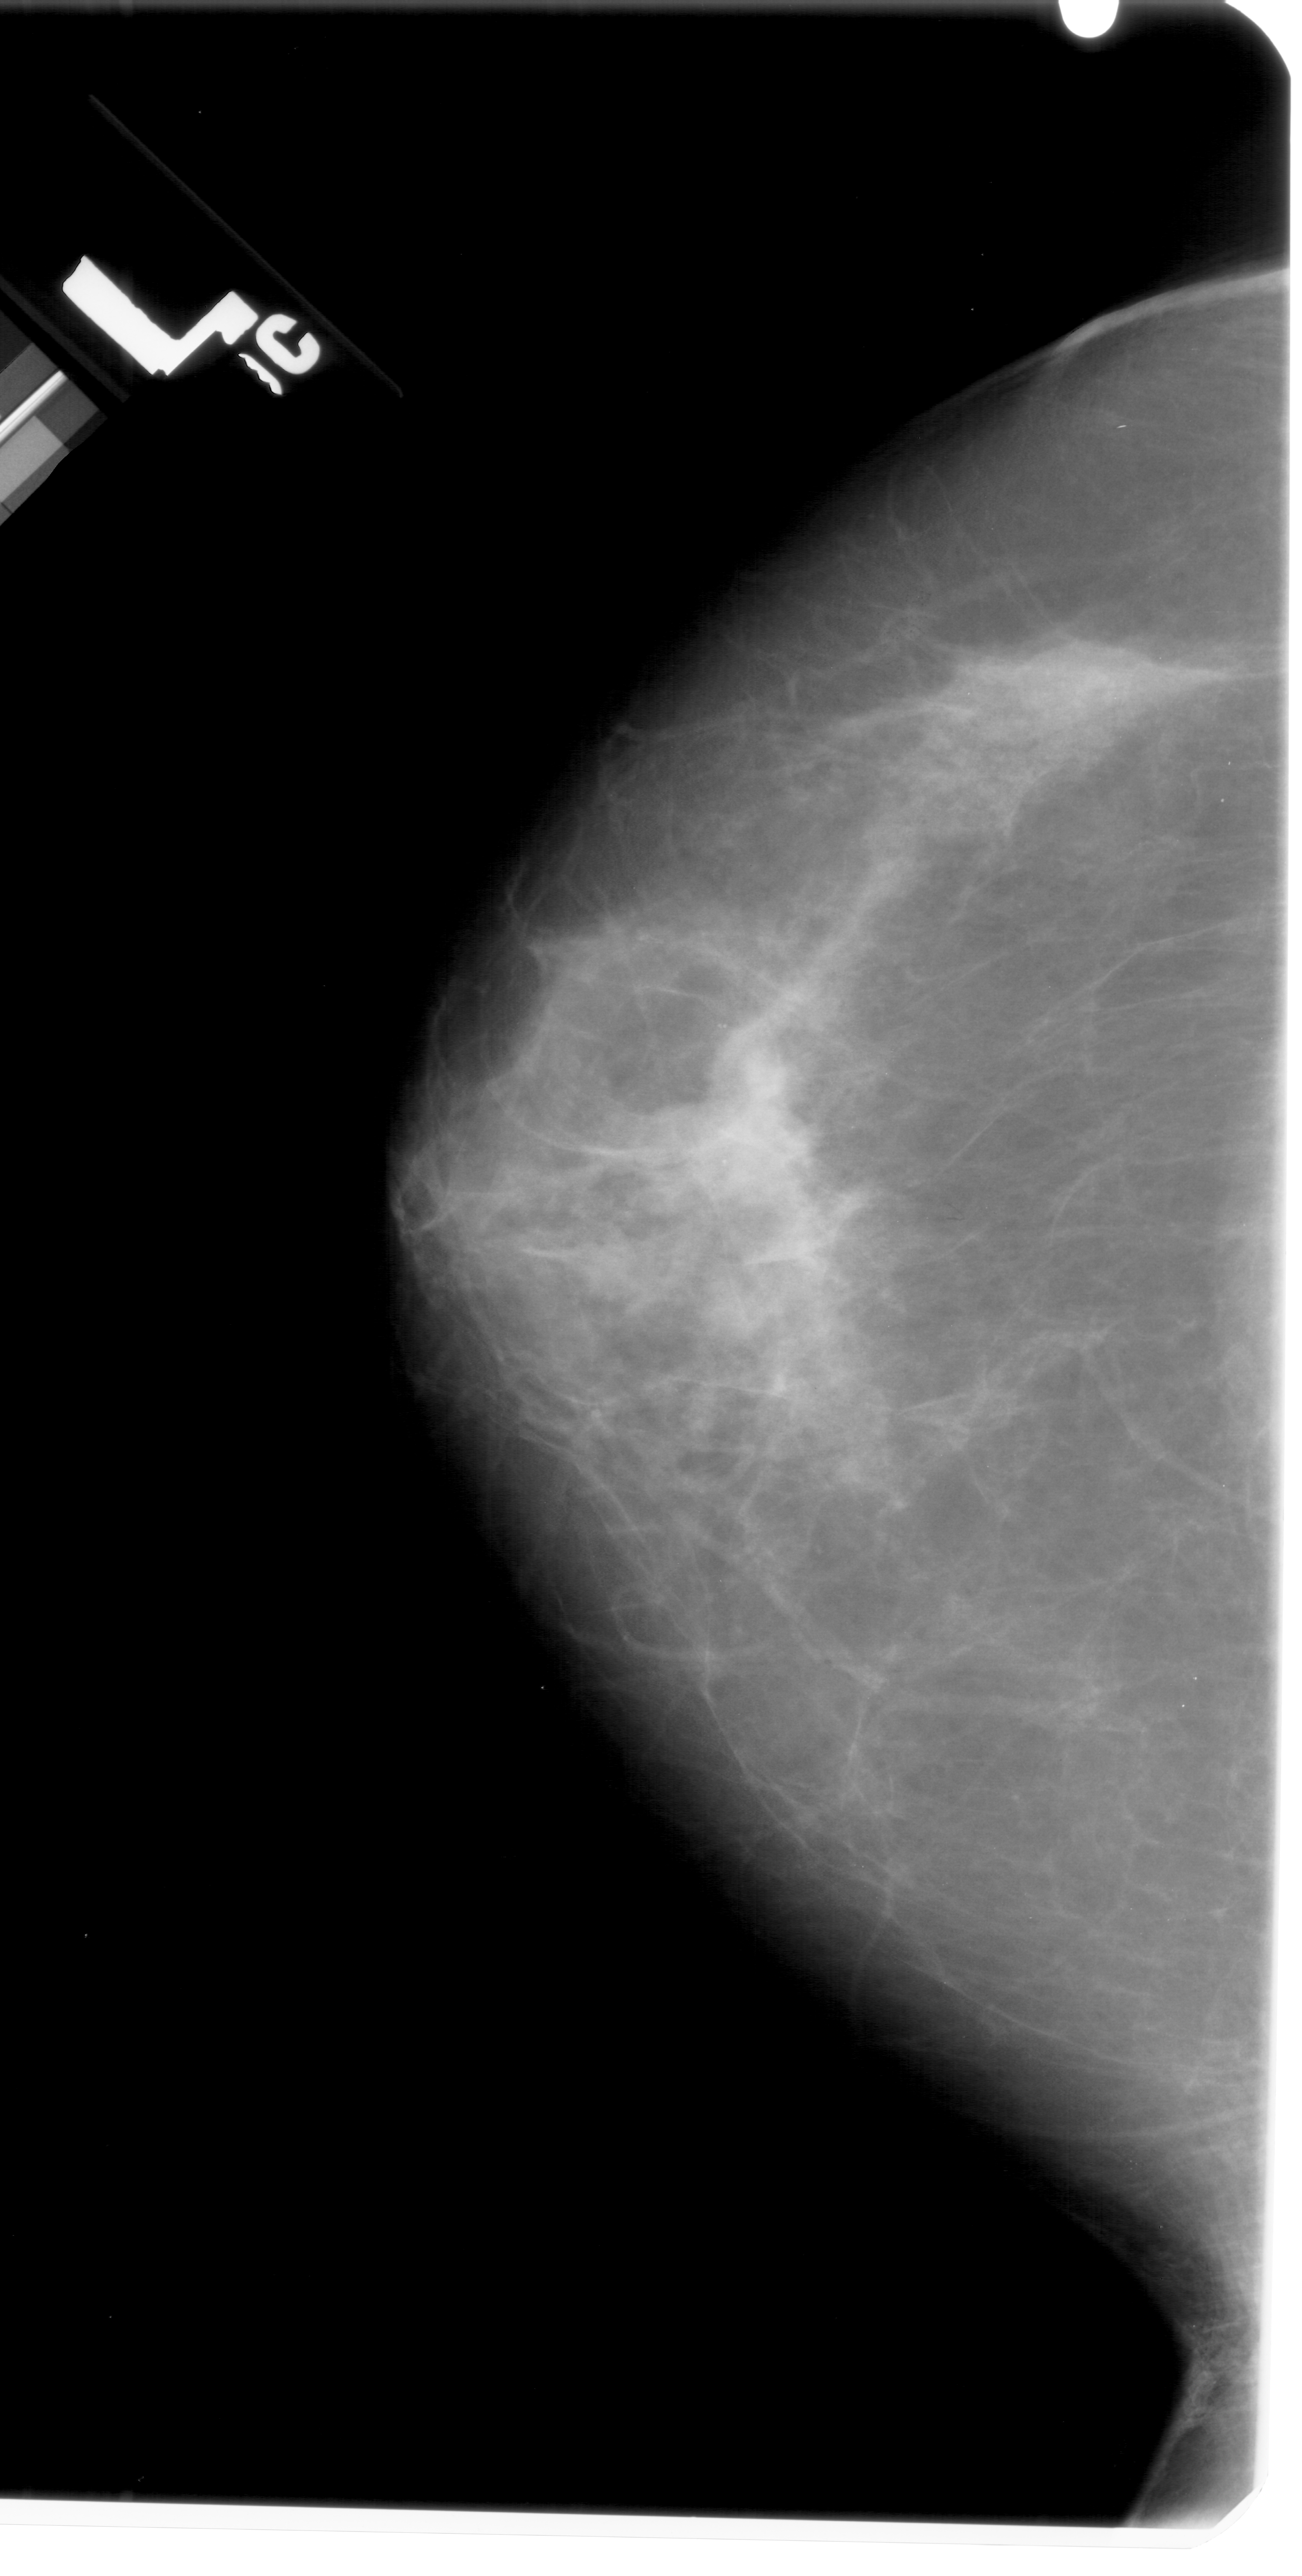
Scanned film-screen mammogram. Left breast. CC view. Breast composition: scattered fibroglandular densities (BI-RADS density category 2 of 4). 1302 × 2576 image matrix.
Marked abnormalities (boxes around the expert regions of interest):
- mass, shape irregular, margins ill defined; BI-RADS assessment category 4; pathology (as recorded): malignant: bounding box [x1, y1, x2, y2] px = [666, 1055, 826, 1208]